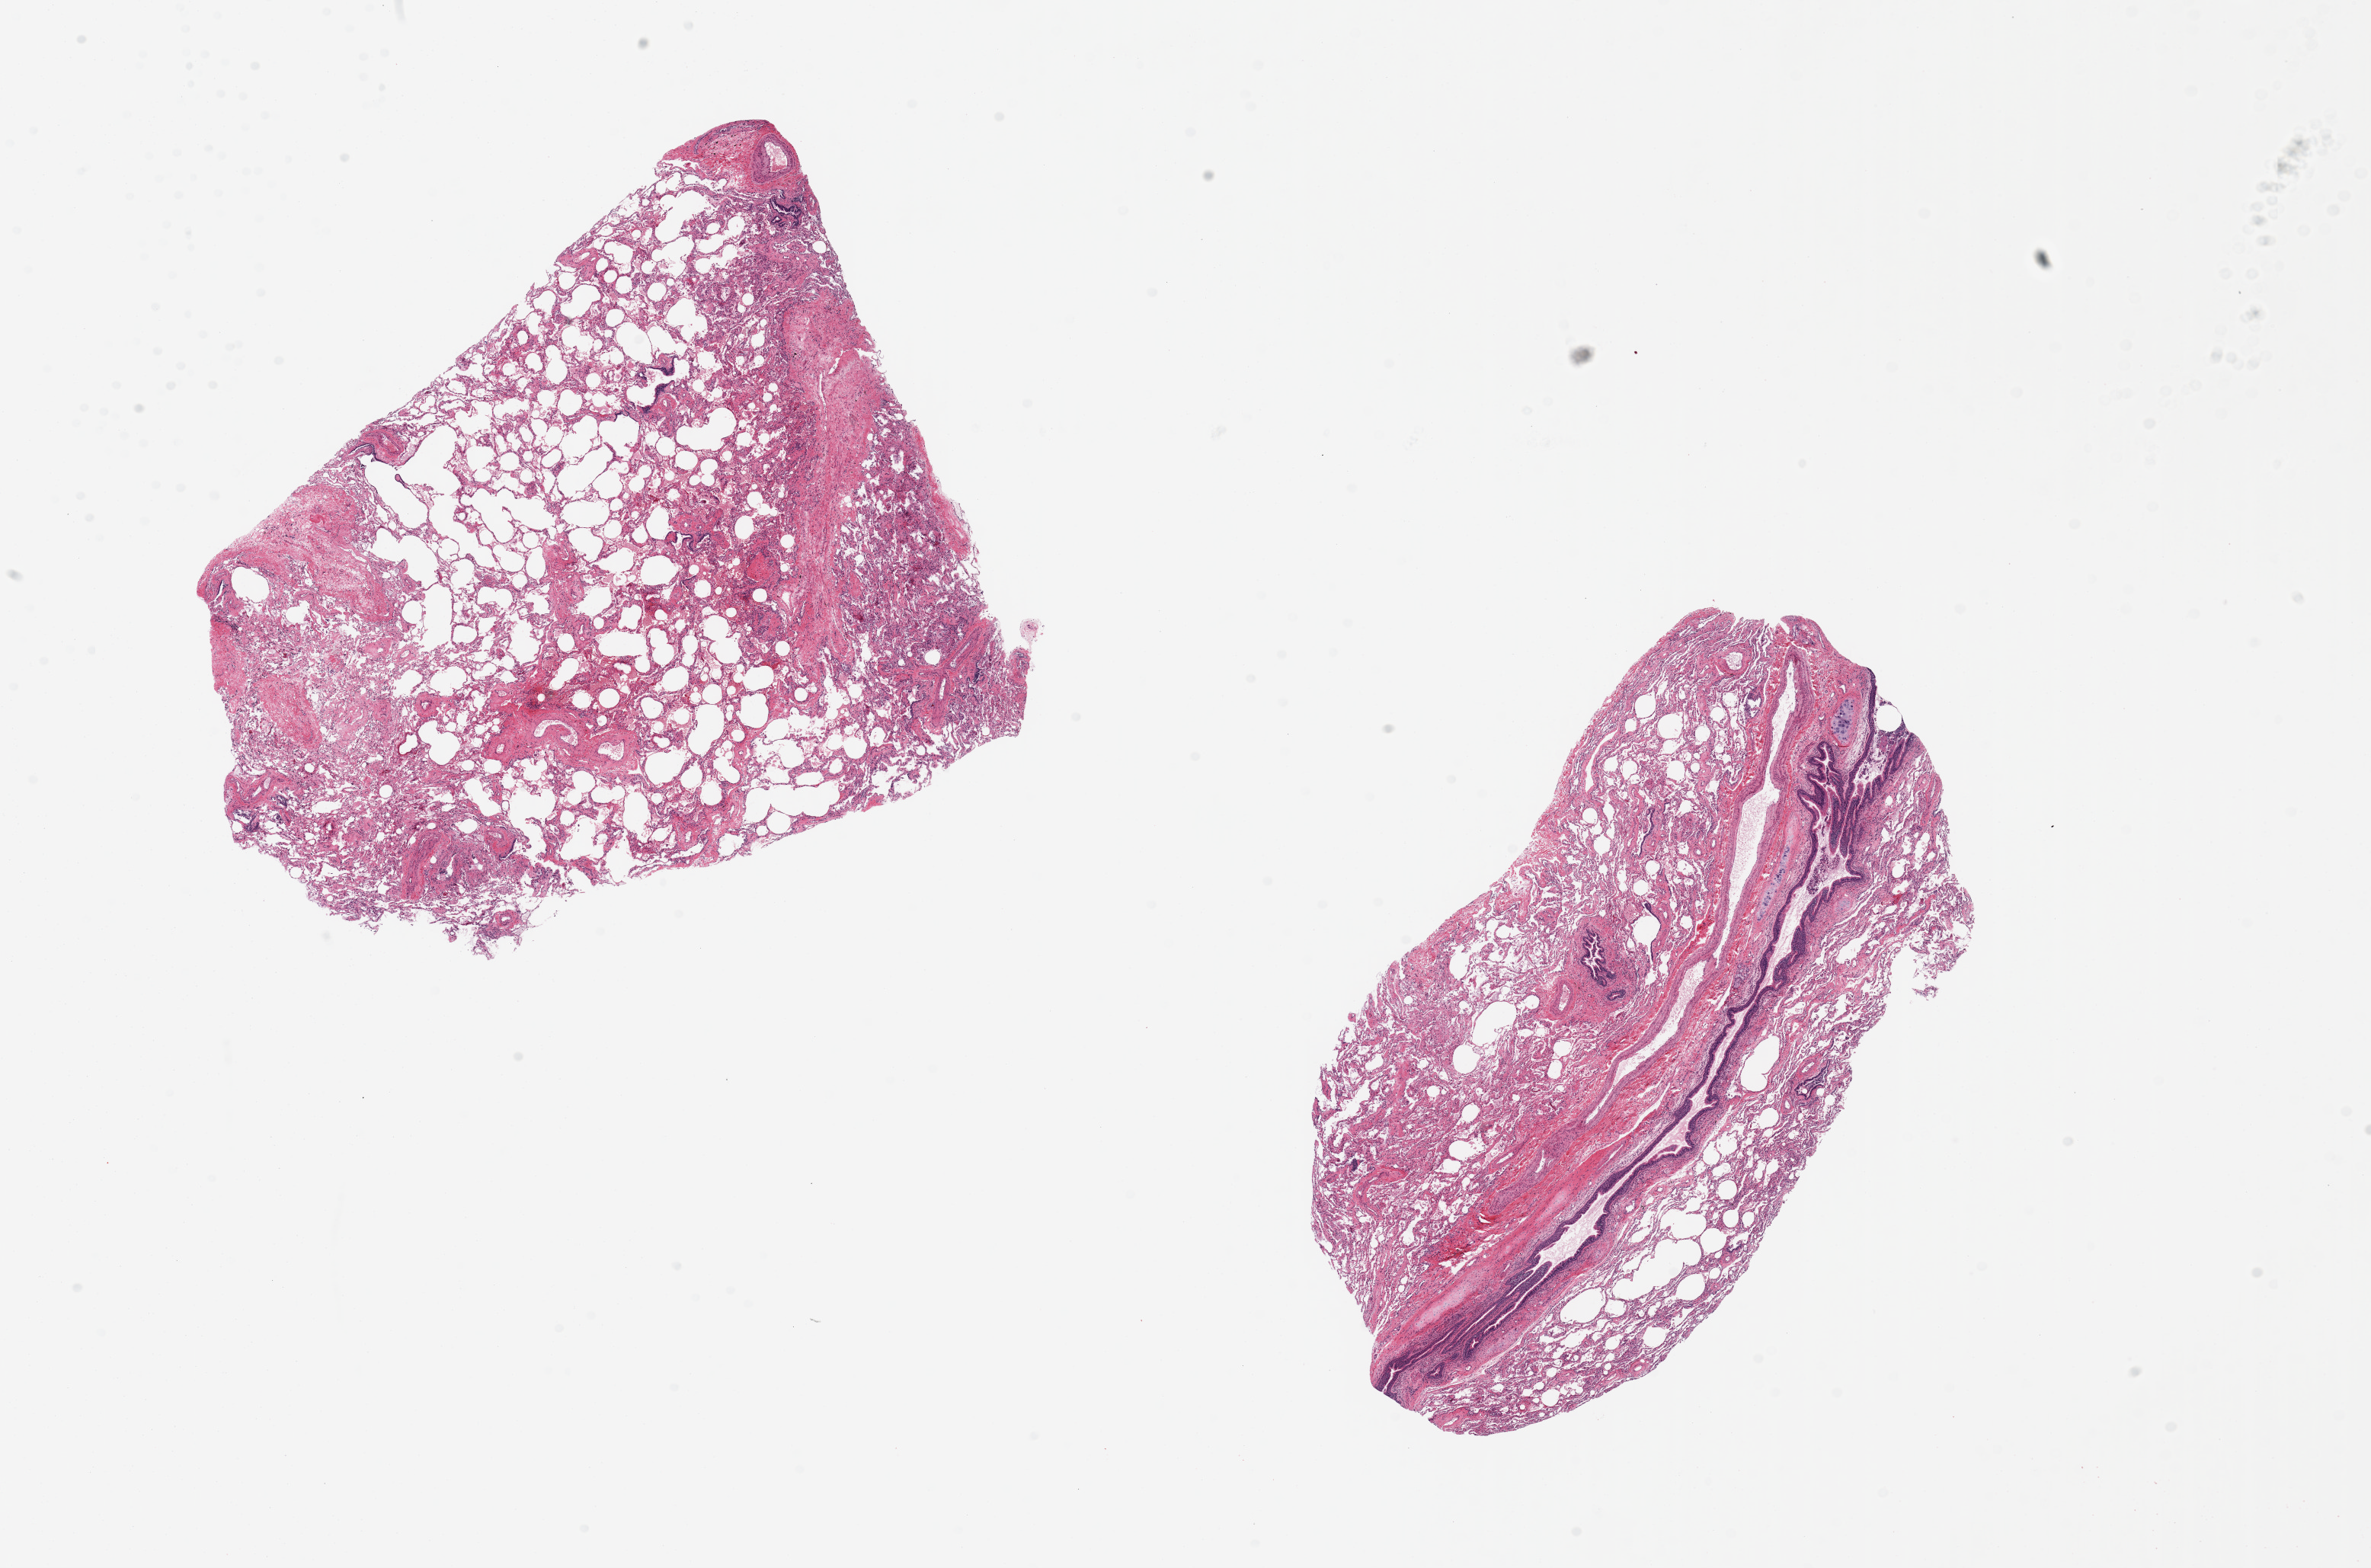
Whole-slide image, haematoxylin and eosin stain — low-resolution overview of the scanned area, about 24.6 x 16.3 mm (acquisition: 20x scan), PAXgene-fixed paraffin-embedded (PFPE) section, section of lung (target tissue), tissue donor sample. Donor: female.
• pathologist's review note for this sample: 2 pieces, 9x7 & 9x5mm